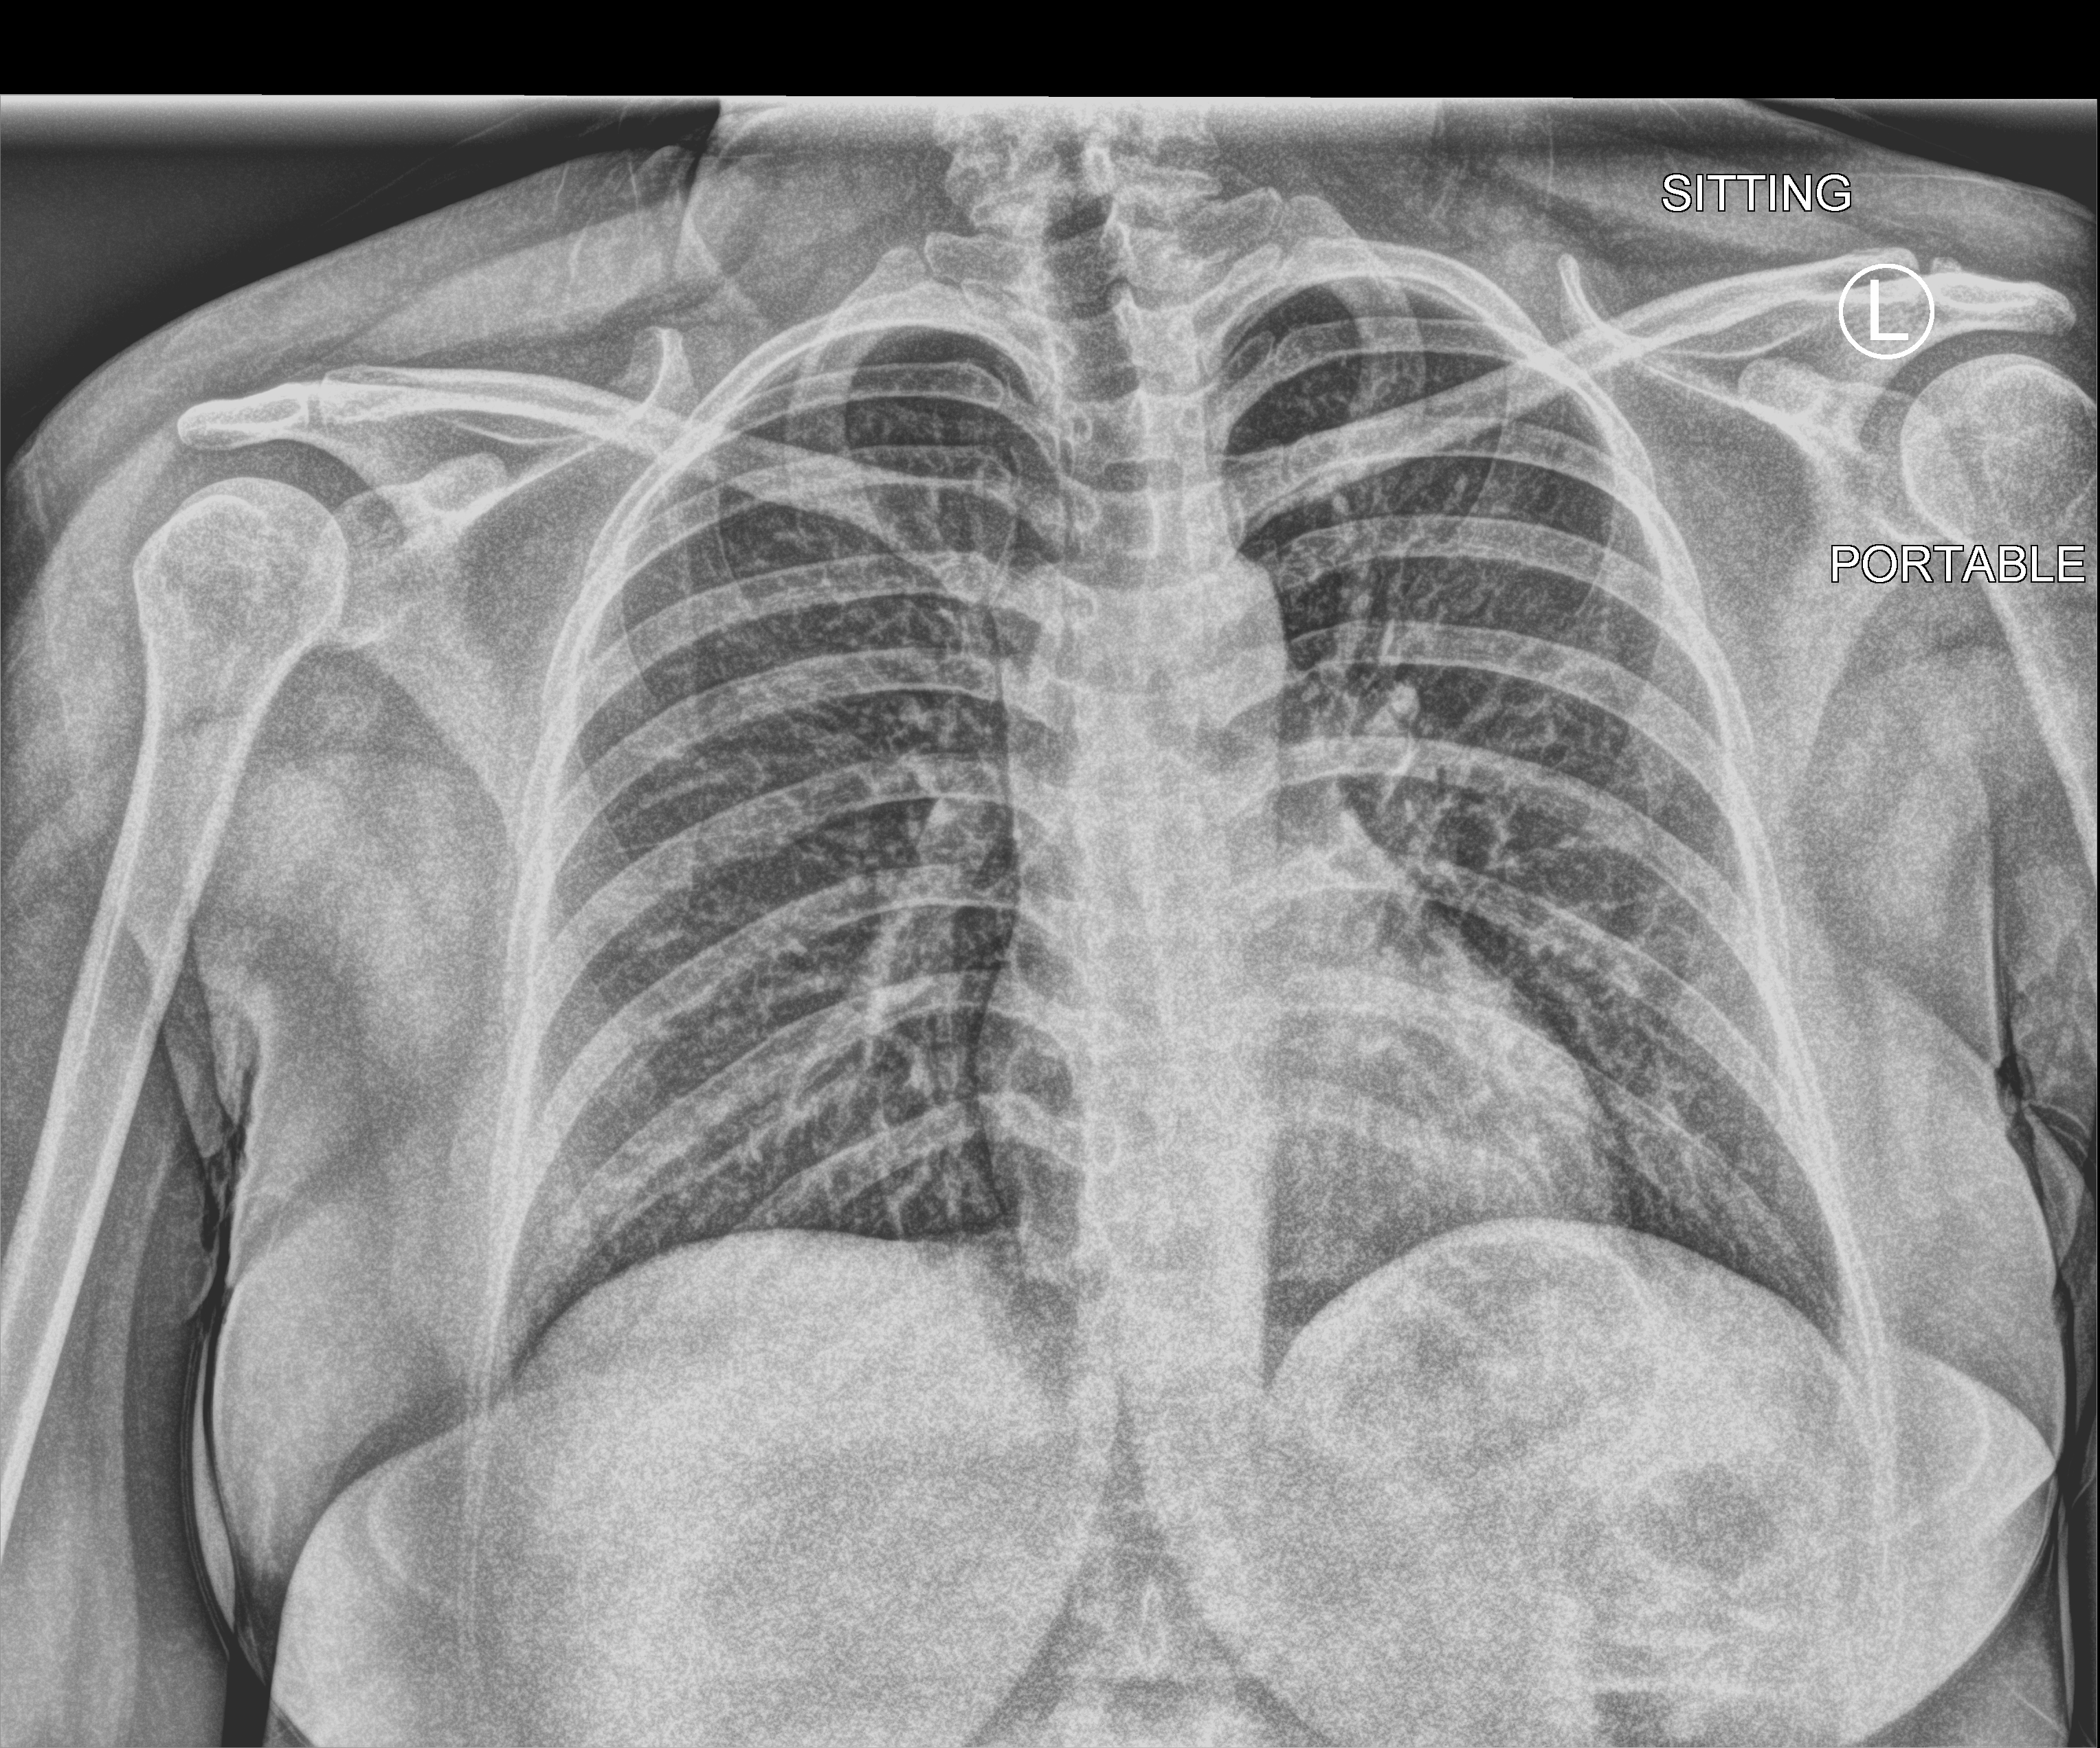
Chest X-ray (portable), anteroposterior (AP) projection. Patient hospitalised with COVID-19; female, aged 18–59 years.
Hospital-stay facts (about this admission, not read from this image; timing relative to this image not recorded): admitted to intensive care during this hospital stay: no; smoking status (admission record): never; other chronic lung disease (admission record): yes.